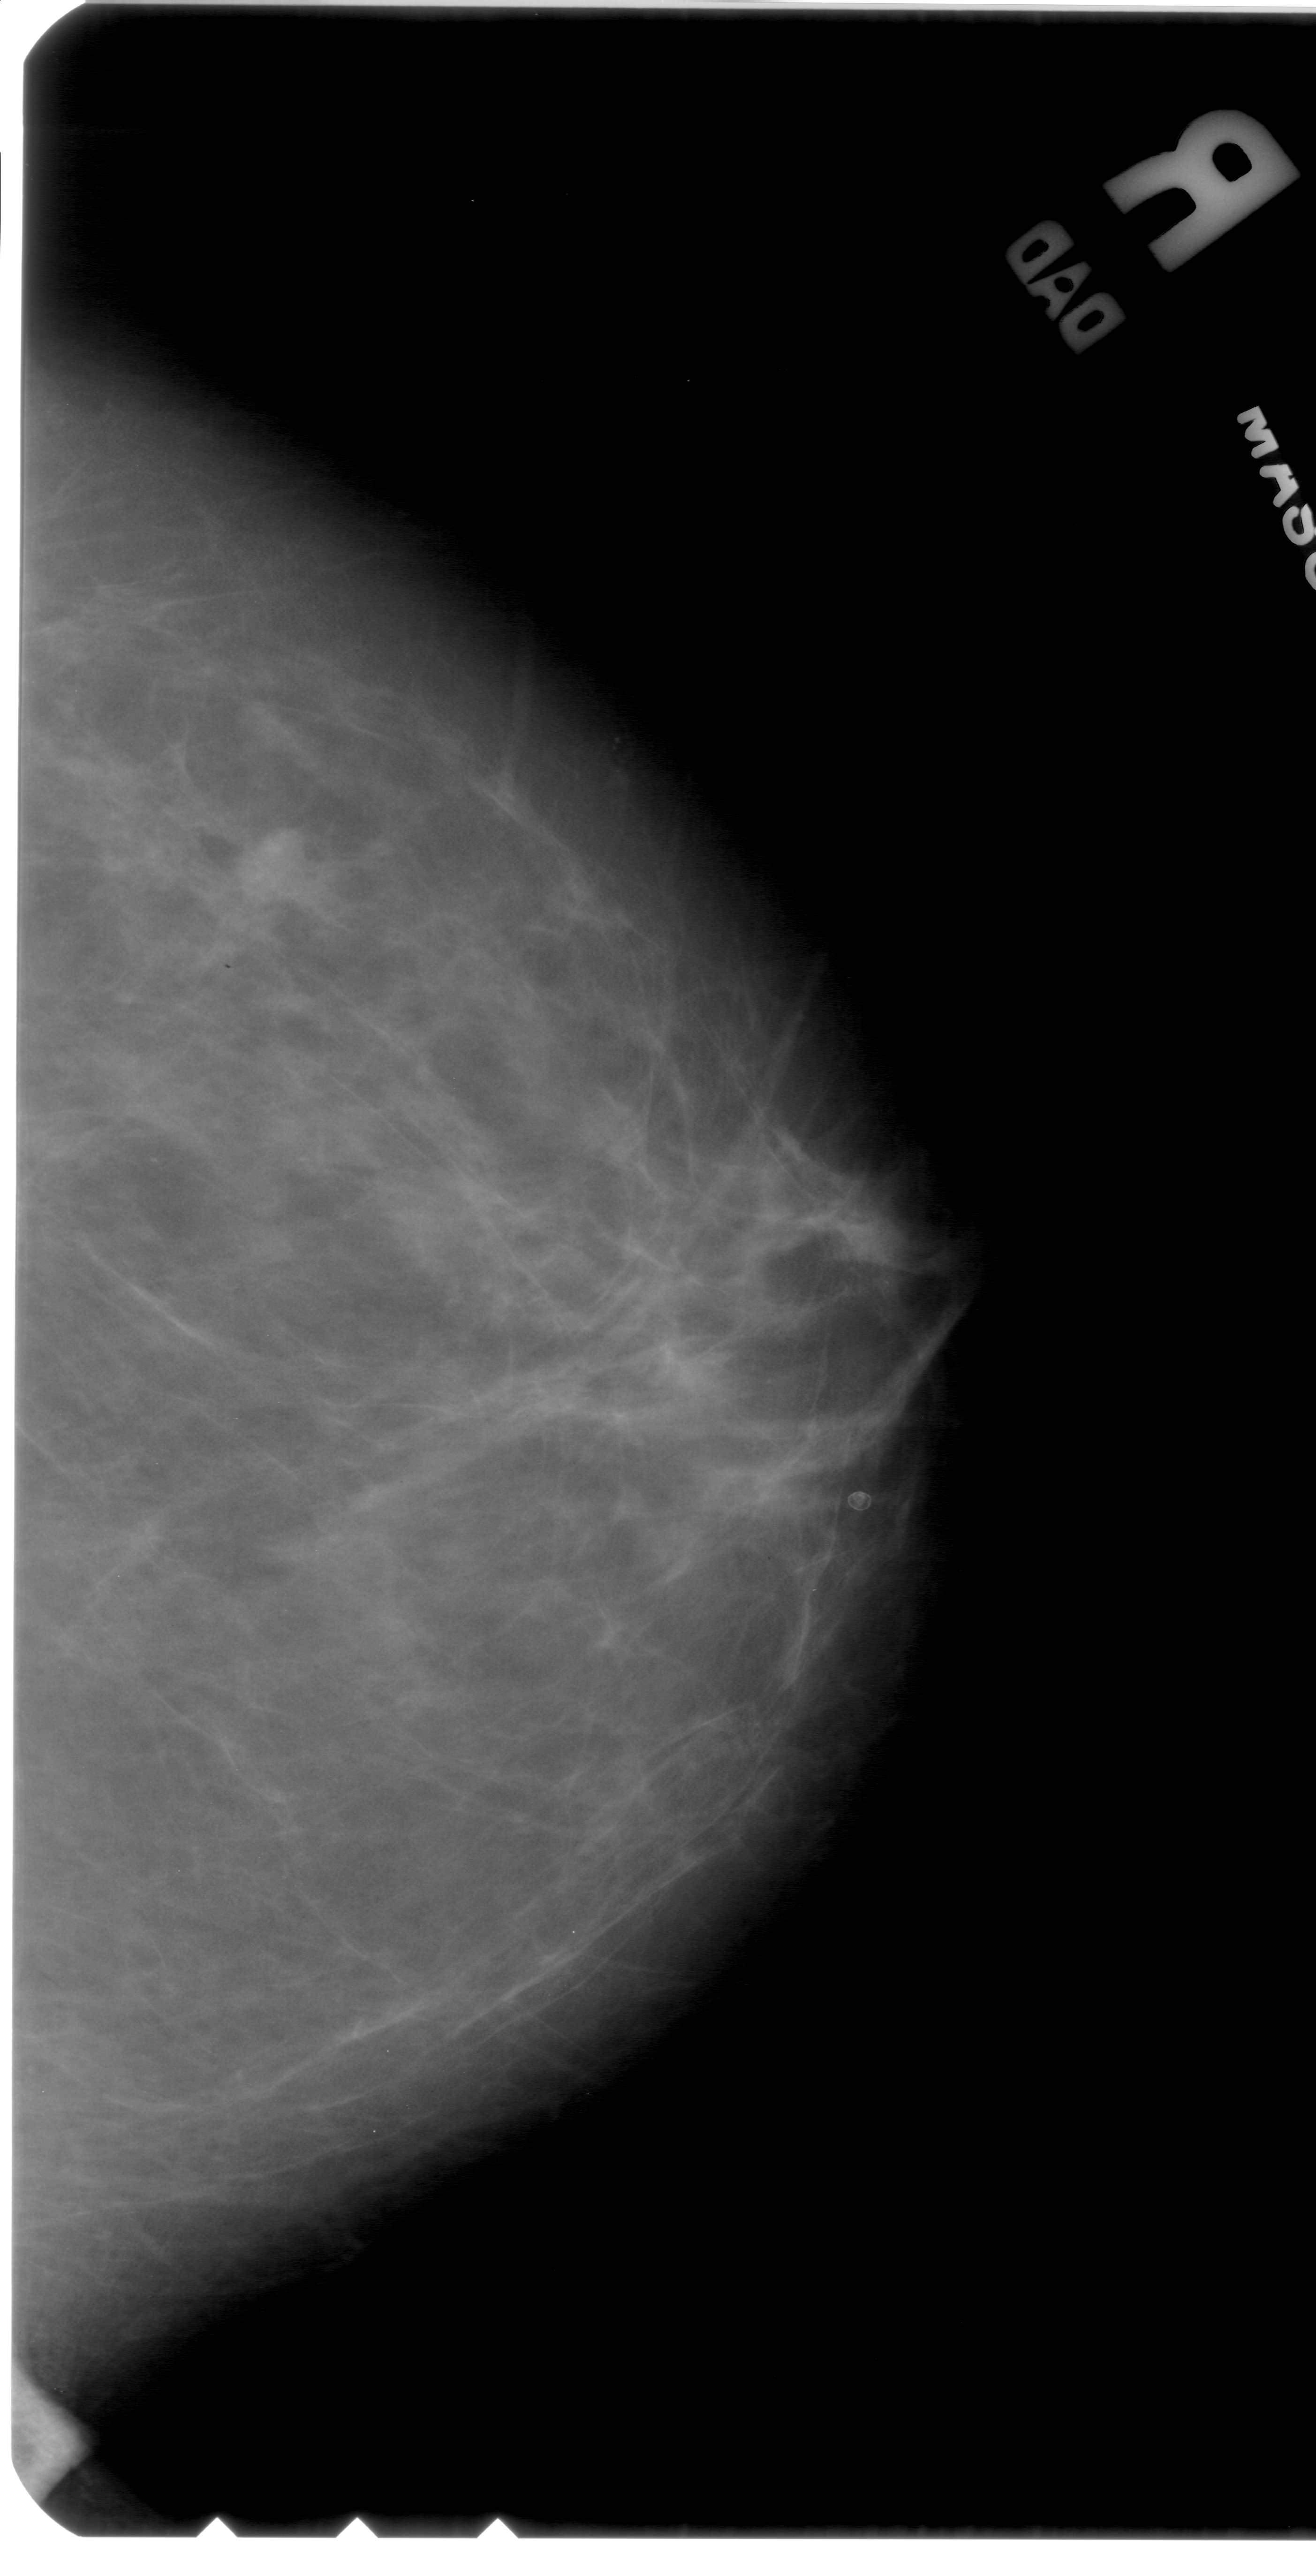
Mammogram (digitized film), right breast, CC view, BI-RADS breast density category 2 (scale 1–4).
Marked abnormality: mass, shape lobulated, margins obscured; BI-RADS assessment category 4; pathology (as recorded): malignant.